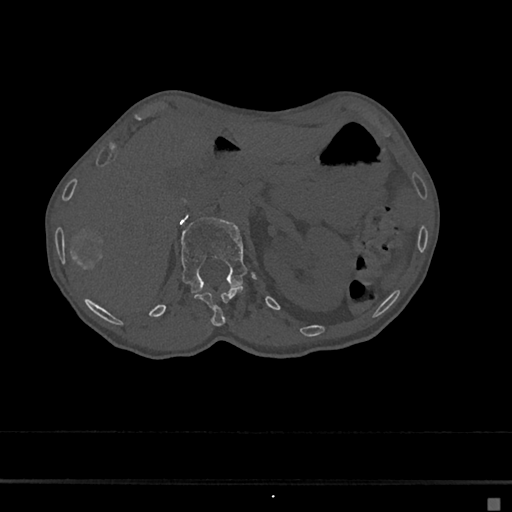
CT including the spine, one axial slice; reconstruction kernel Br40s/3; 120 kVp; bone window (W 1800 / L 400 HU); 0.5 mm slice thickness; 512 × 512 image matrix, field of view 360 × 360 mm. Patient: female, 68 years. From the clinical record (not read from this slice): primary cancer: renal.
Structures marked on this image (semi-automatic segmentation, software-assisted and operator-edited):
- L1 vertebra: bounding box (x1, y1, x2, y2) in pixels: (181, 217, 255, 293)
- T12 vertebra: (193, 287, 243, 327)